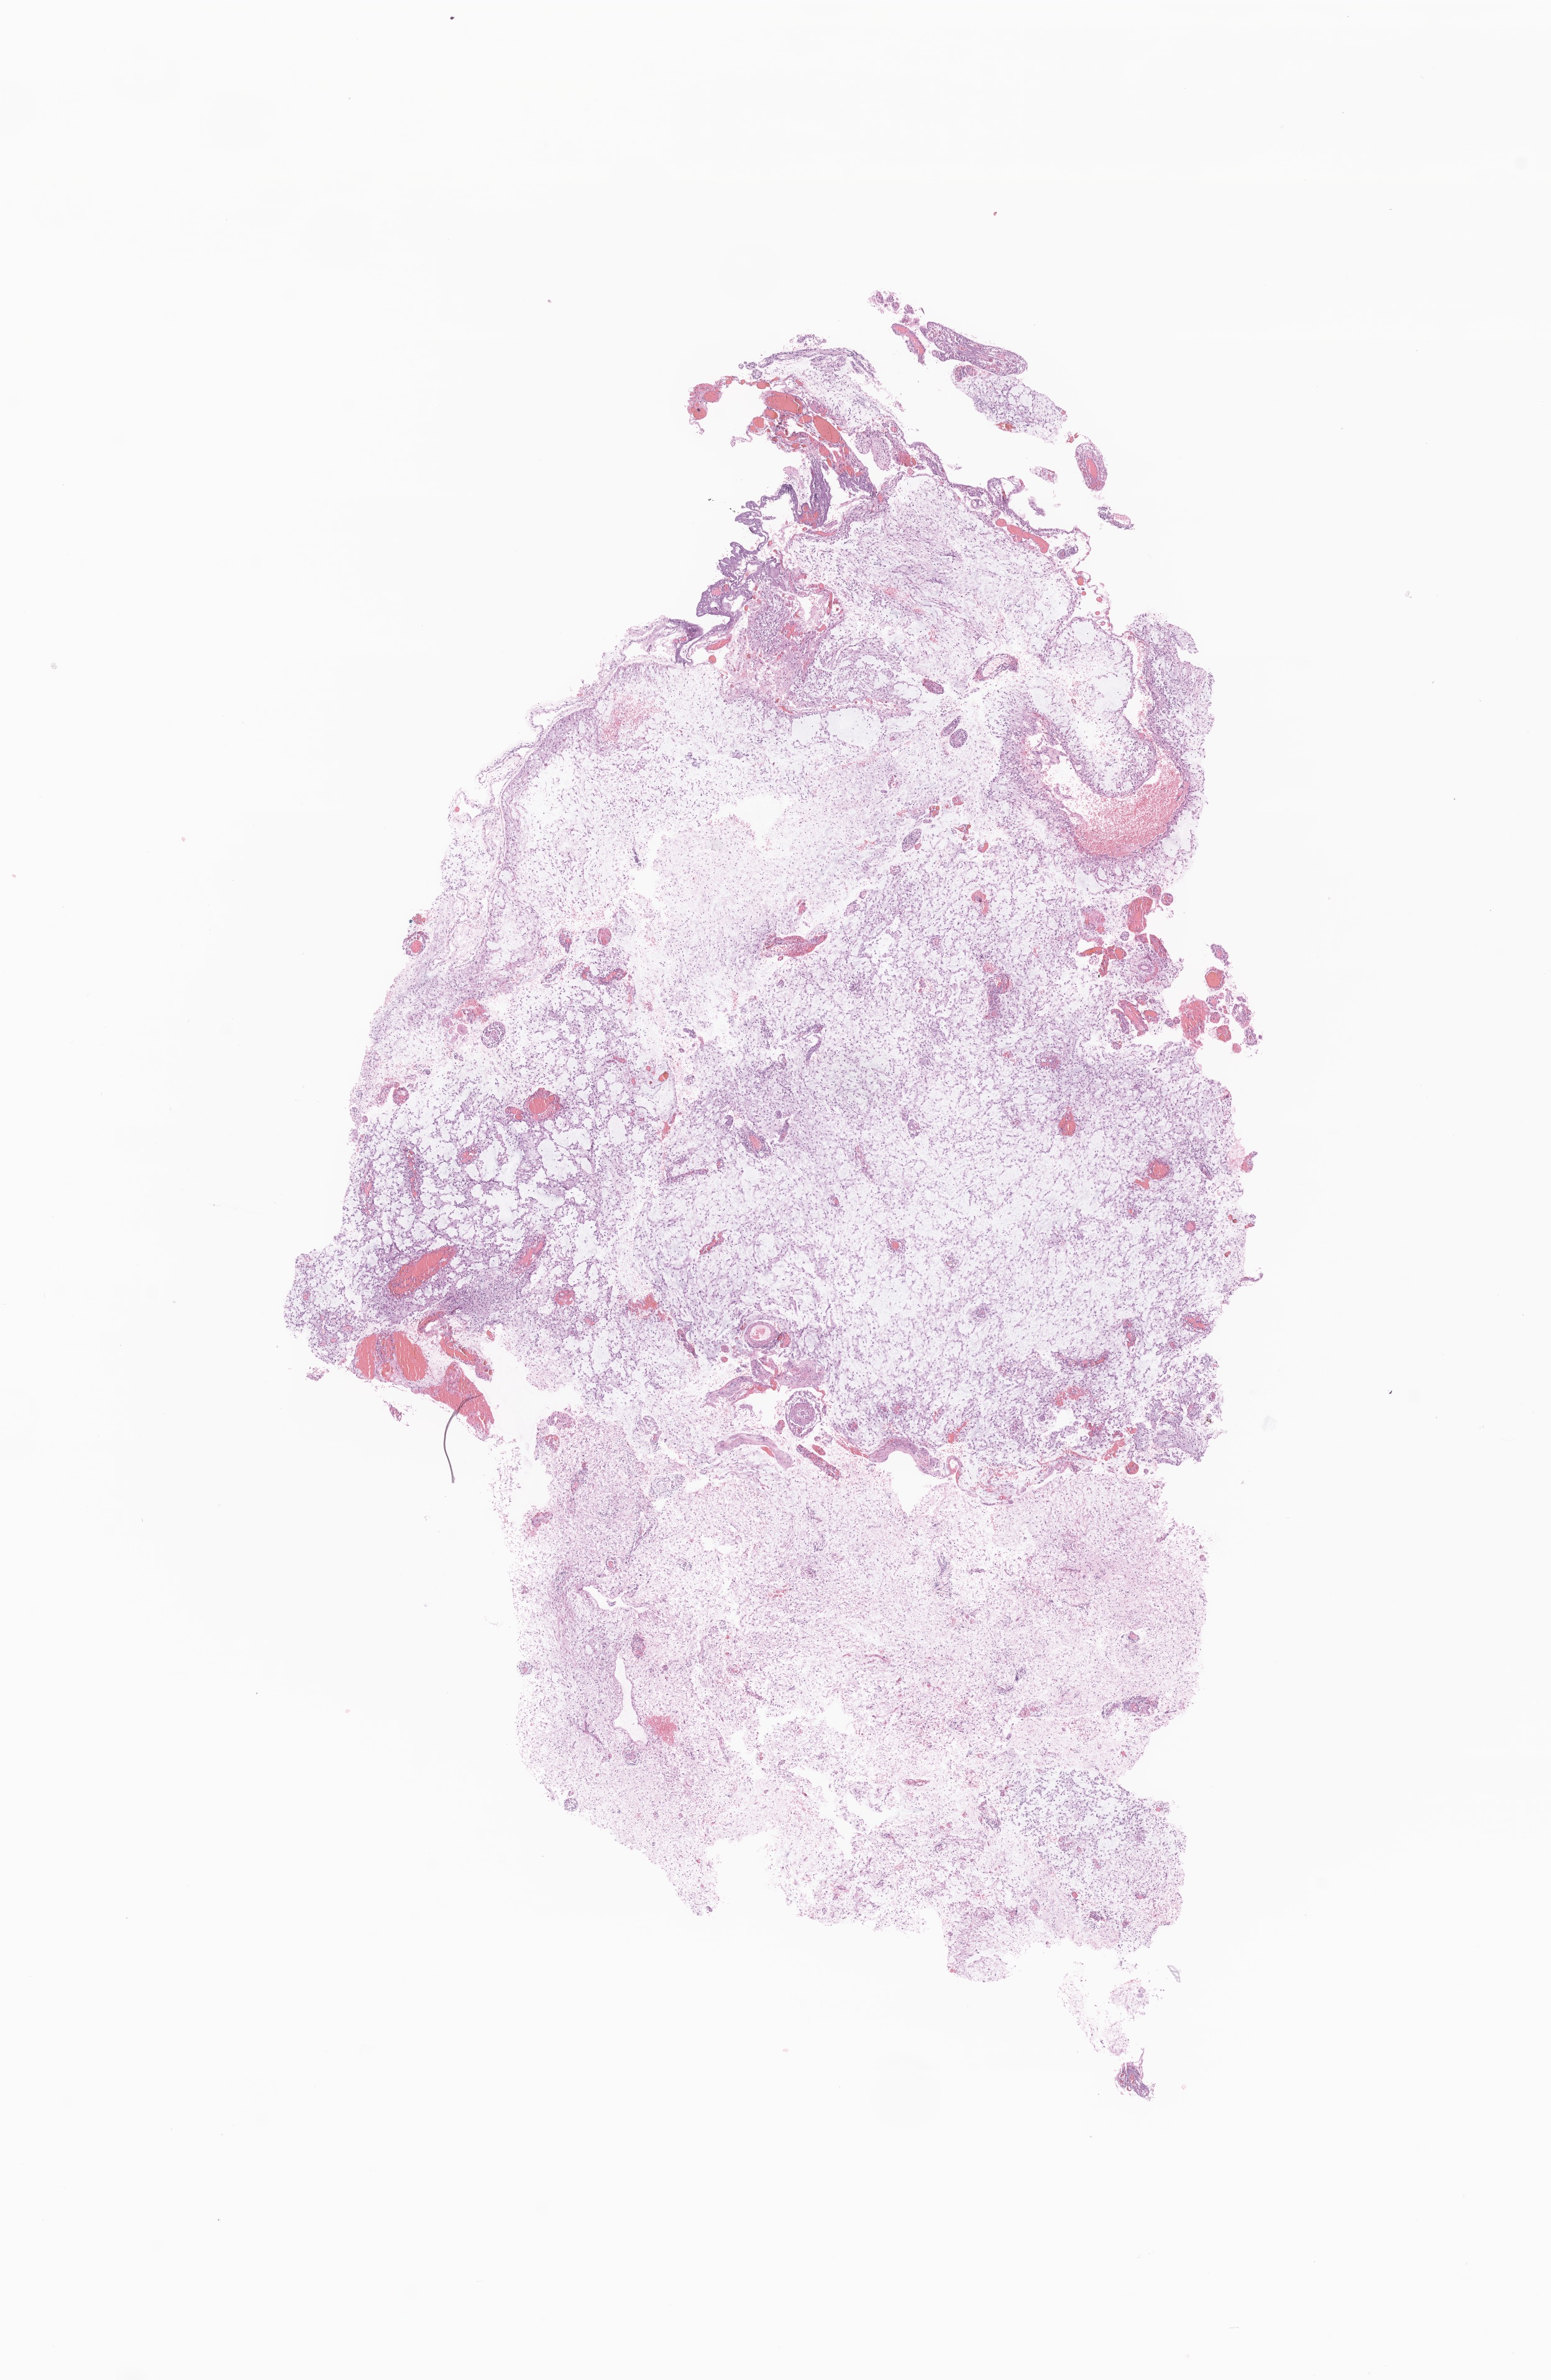
H&E whole-slide image of tumor tissue from the brain — whole scanned area (about 10.5 x 16.2 mm) shown as a low-resolution overview; formalin-fixed paraffin-embedded section. Patient: male, age 106 months (8 years 10 months).
- diagnosis: Astrocytoma, NOS